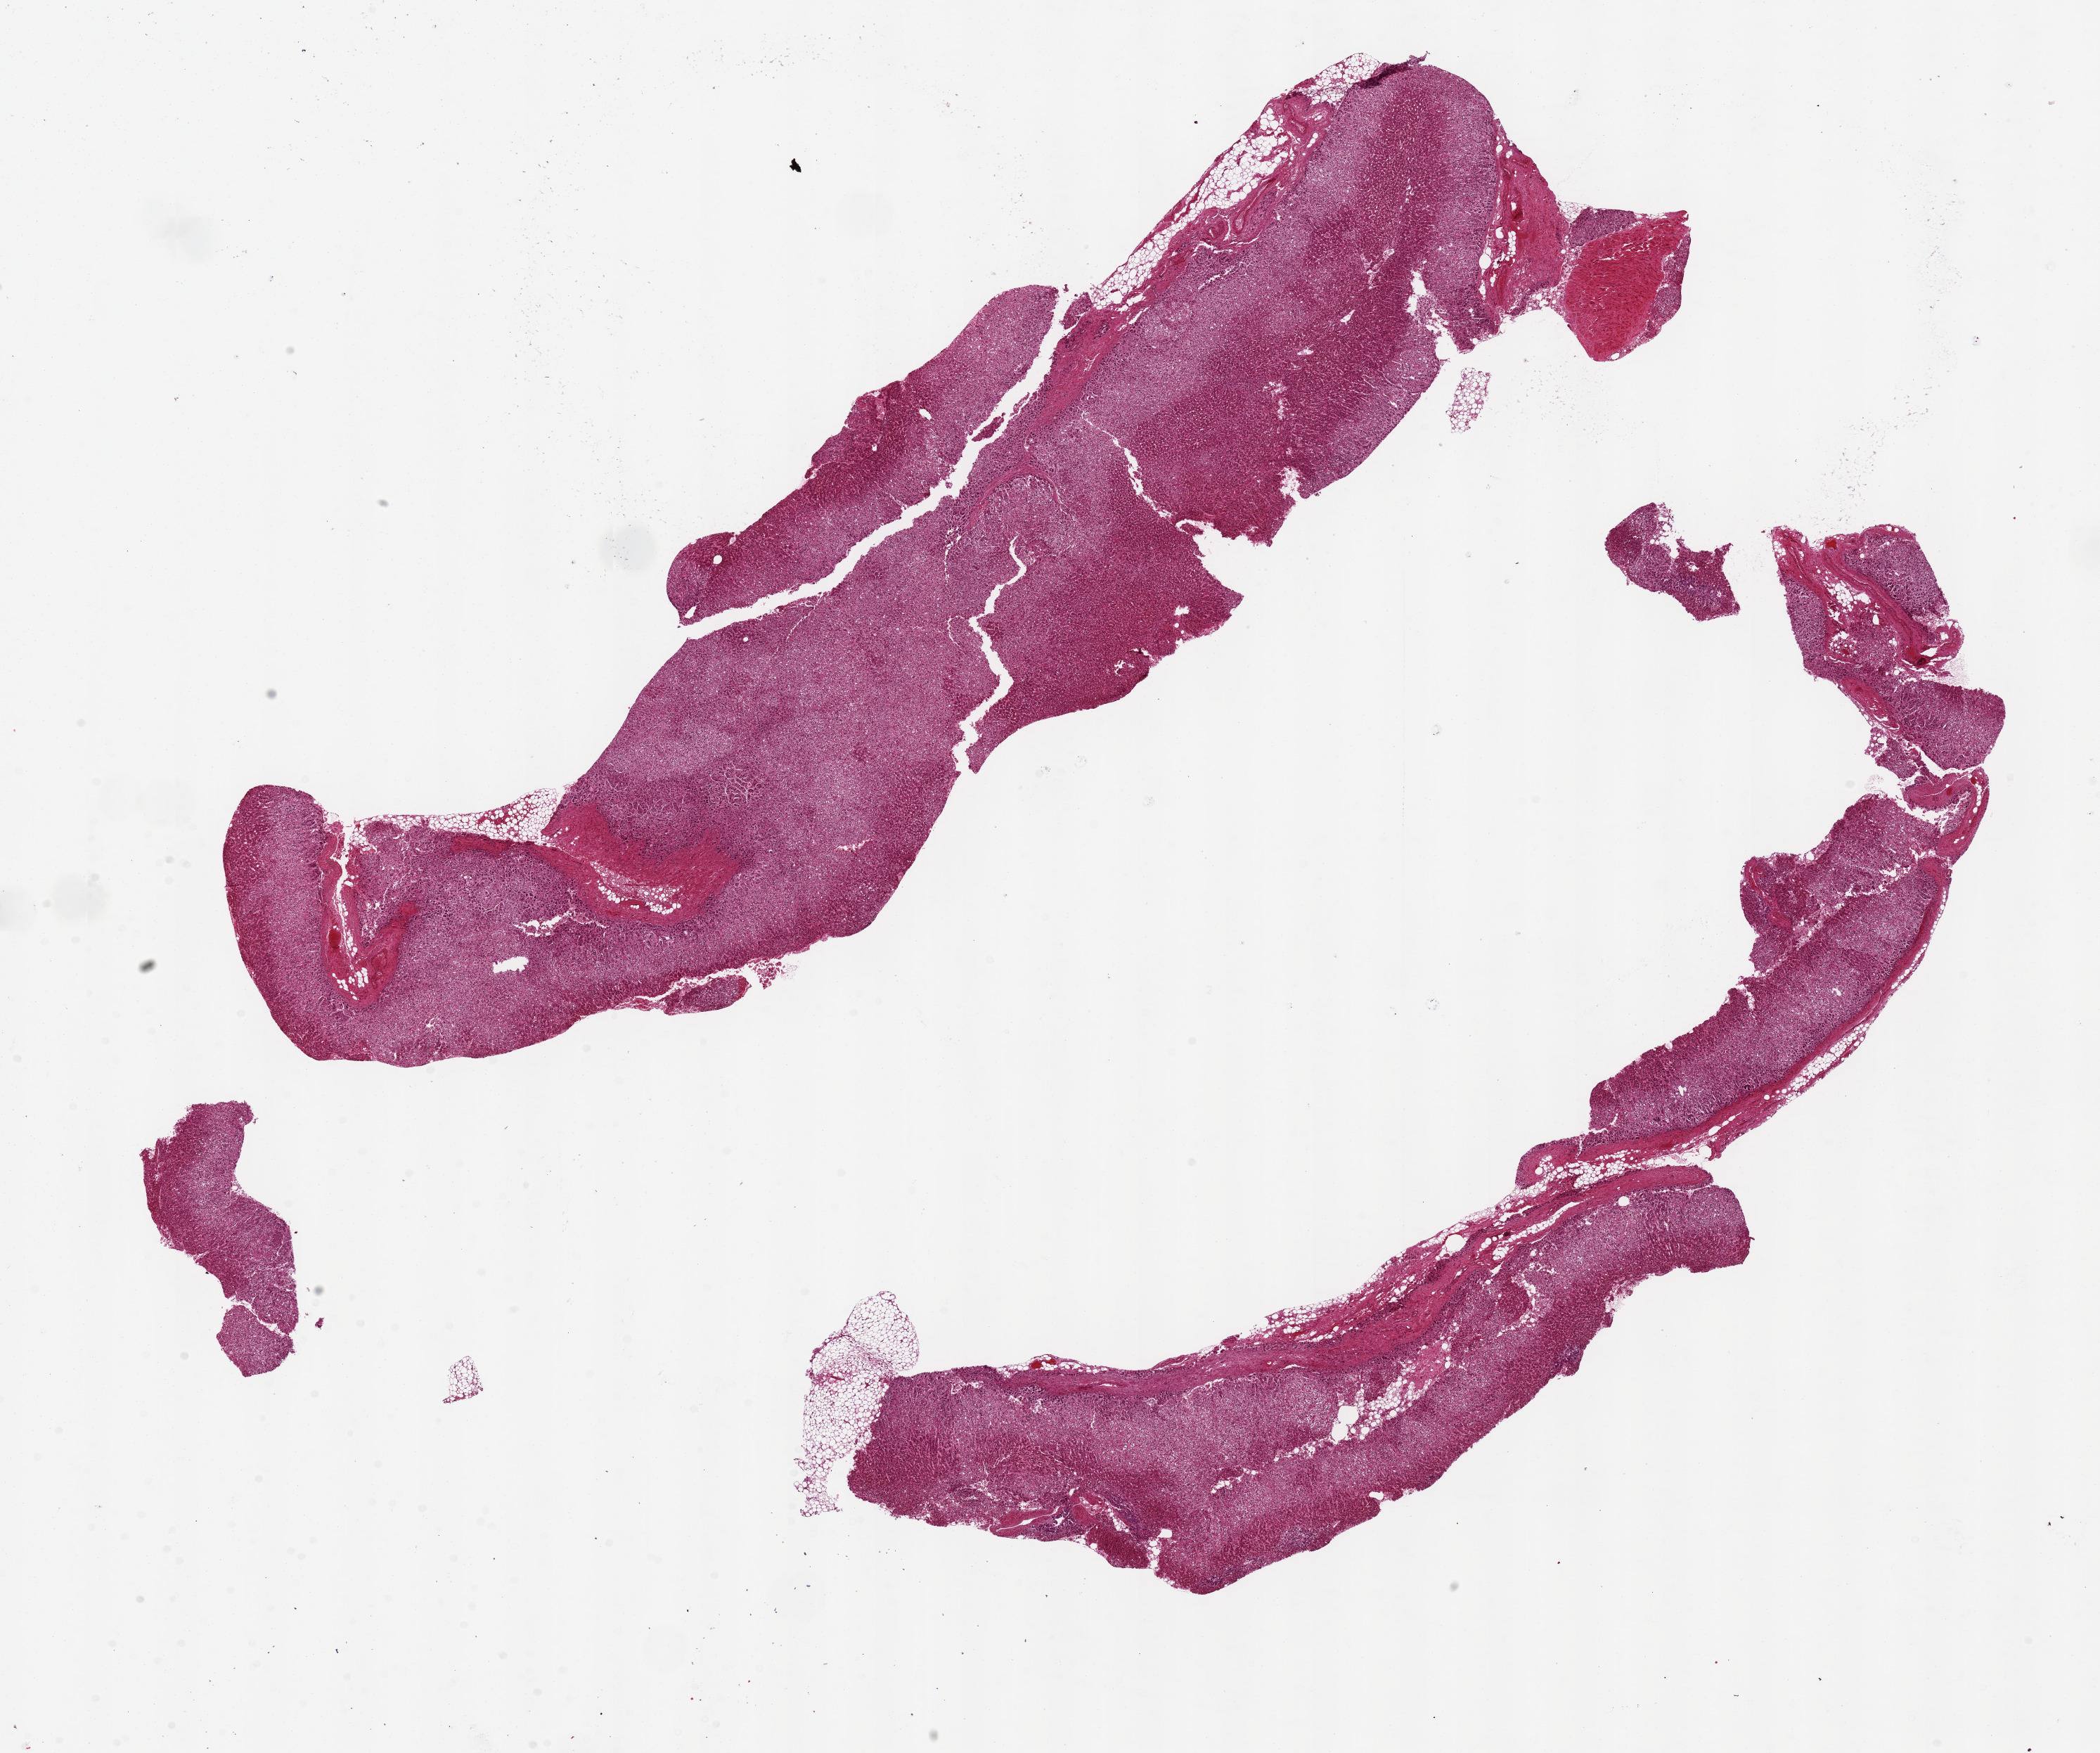
Haematoxylin and eosin whole-slide image, brightfield, low-resolution overview of the scanned area, about 23.6 x 19.7 mm (acquisition: 20x scan). PAXgene-fixed paraffin-embedded (PFPE) section. Section of adrenal gland (target tissue). Donor tissue sample. Donor: male.
Review note (as recorded): 2 aliquots, ~16x3mm. All cortex.